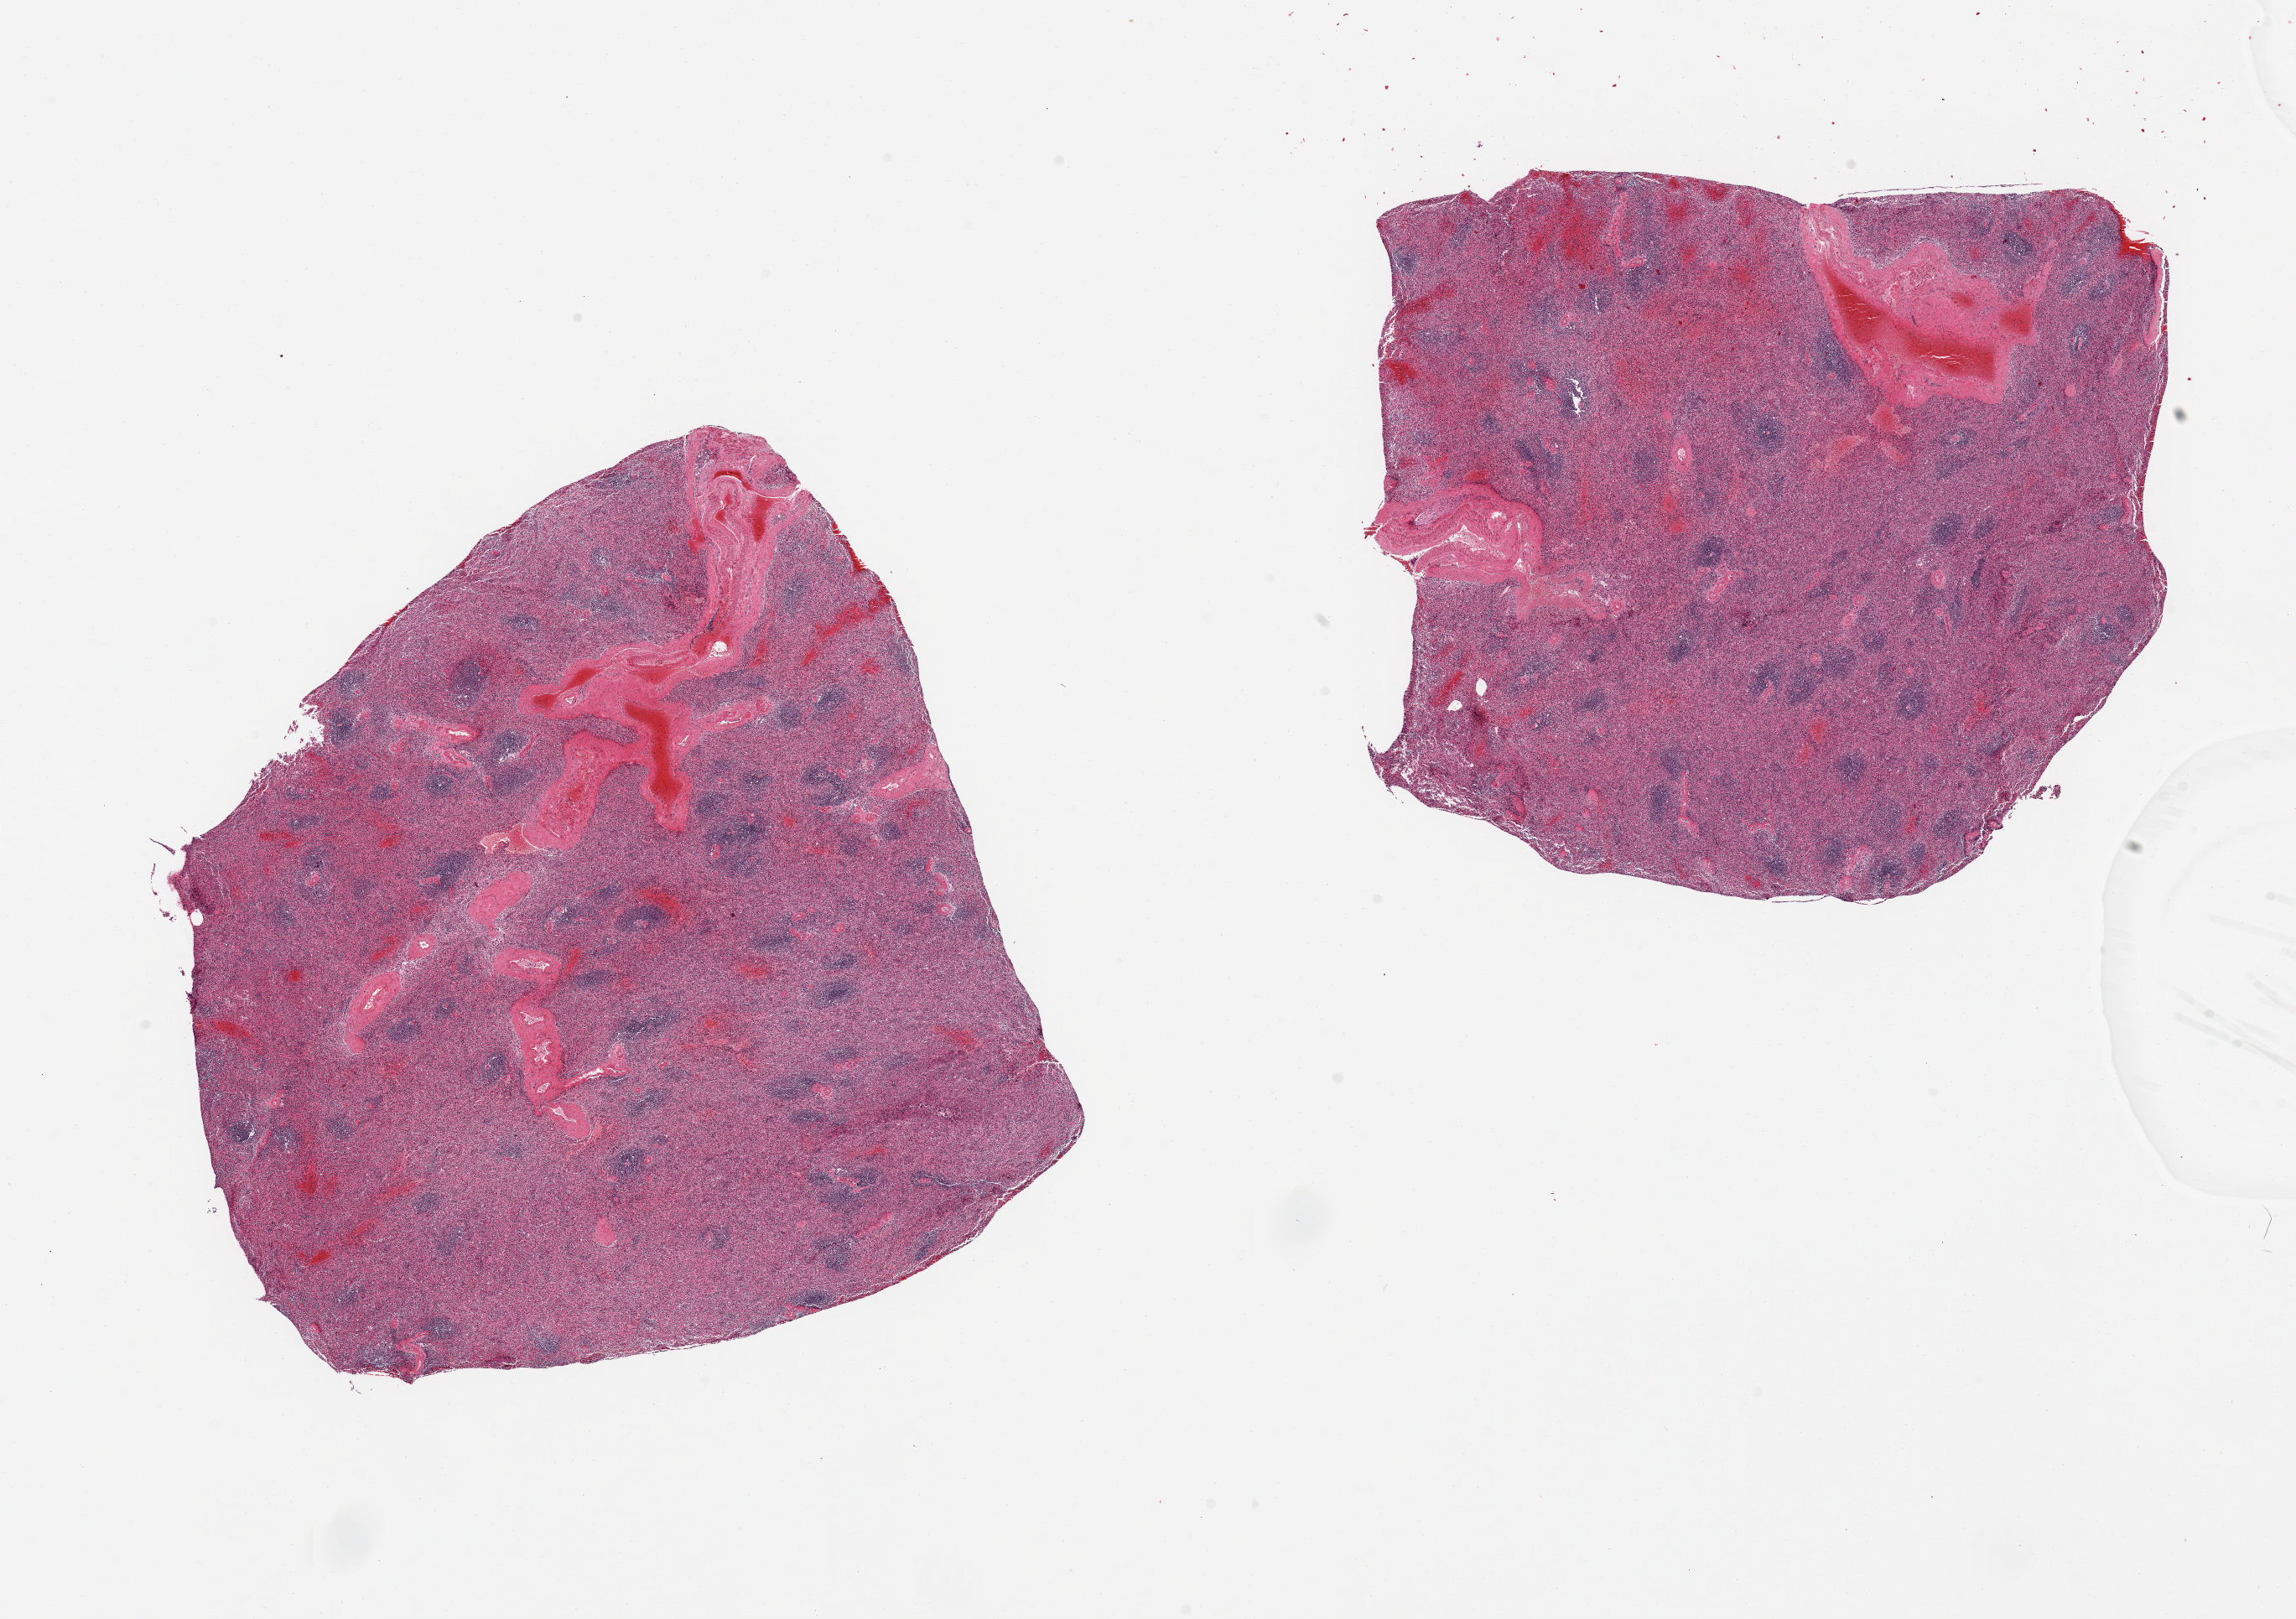
Whole-slide image, haematoxylin and eosin stain, a low-resolution overview of the entire scanned area, about 21.7 x 15.3 mm; PAXgene-fixed, paraffin-embedded tissue; section of spleen (target tissue); donor tissue sample. Female donor.
Pathologist's review note for this sample: 2 pieces, moderate congestion.